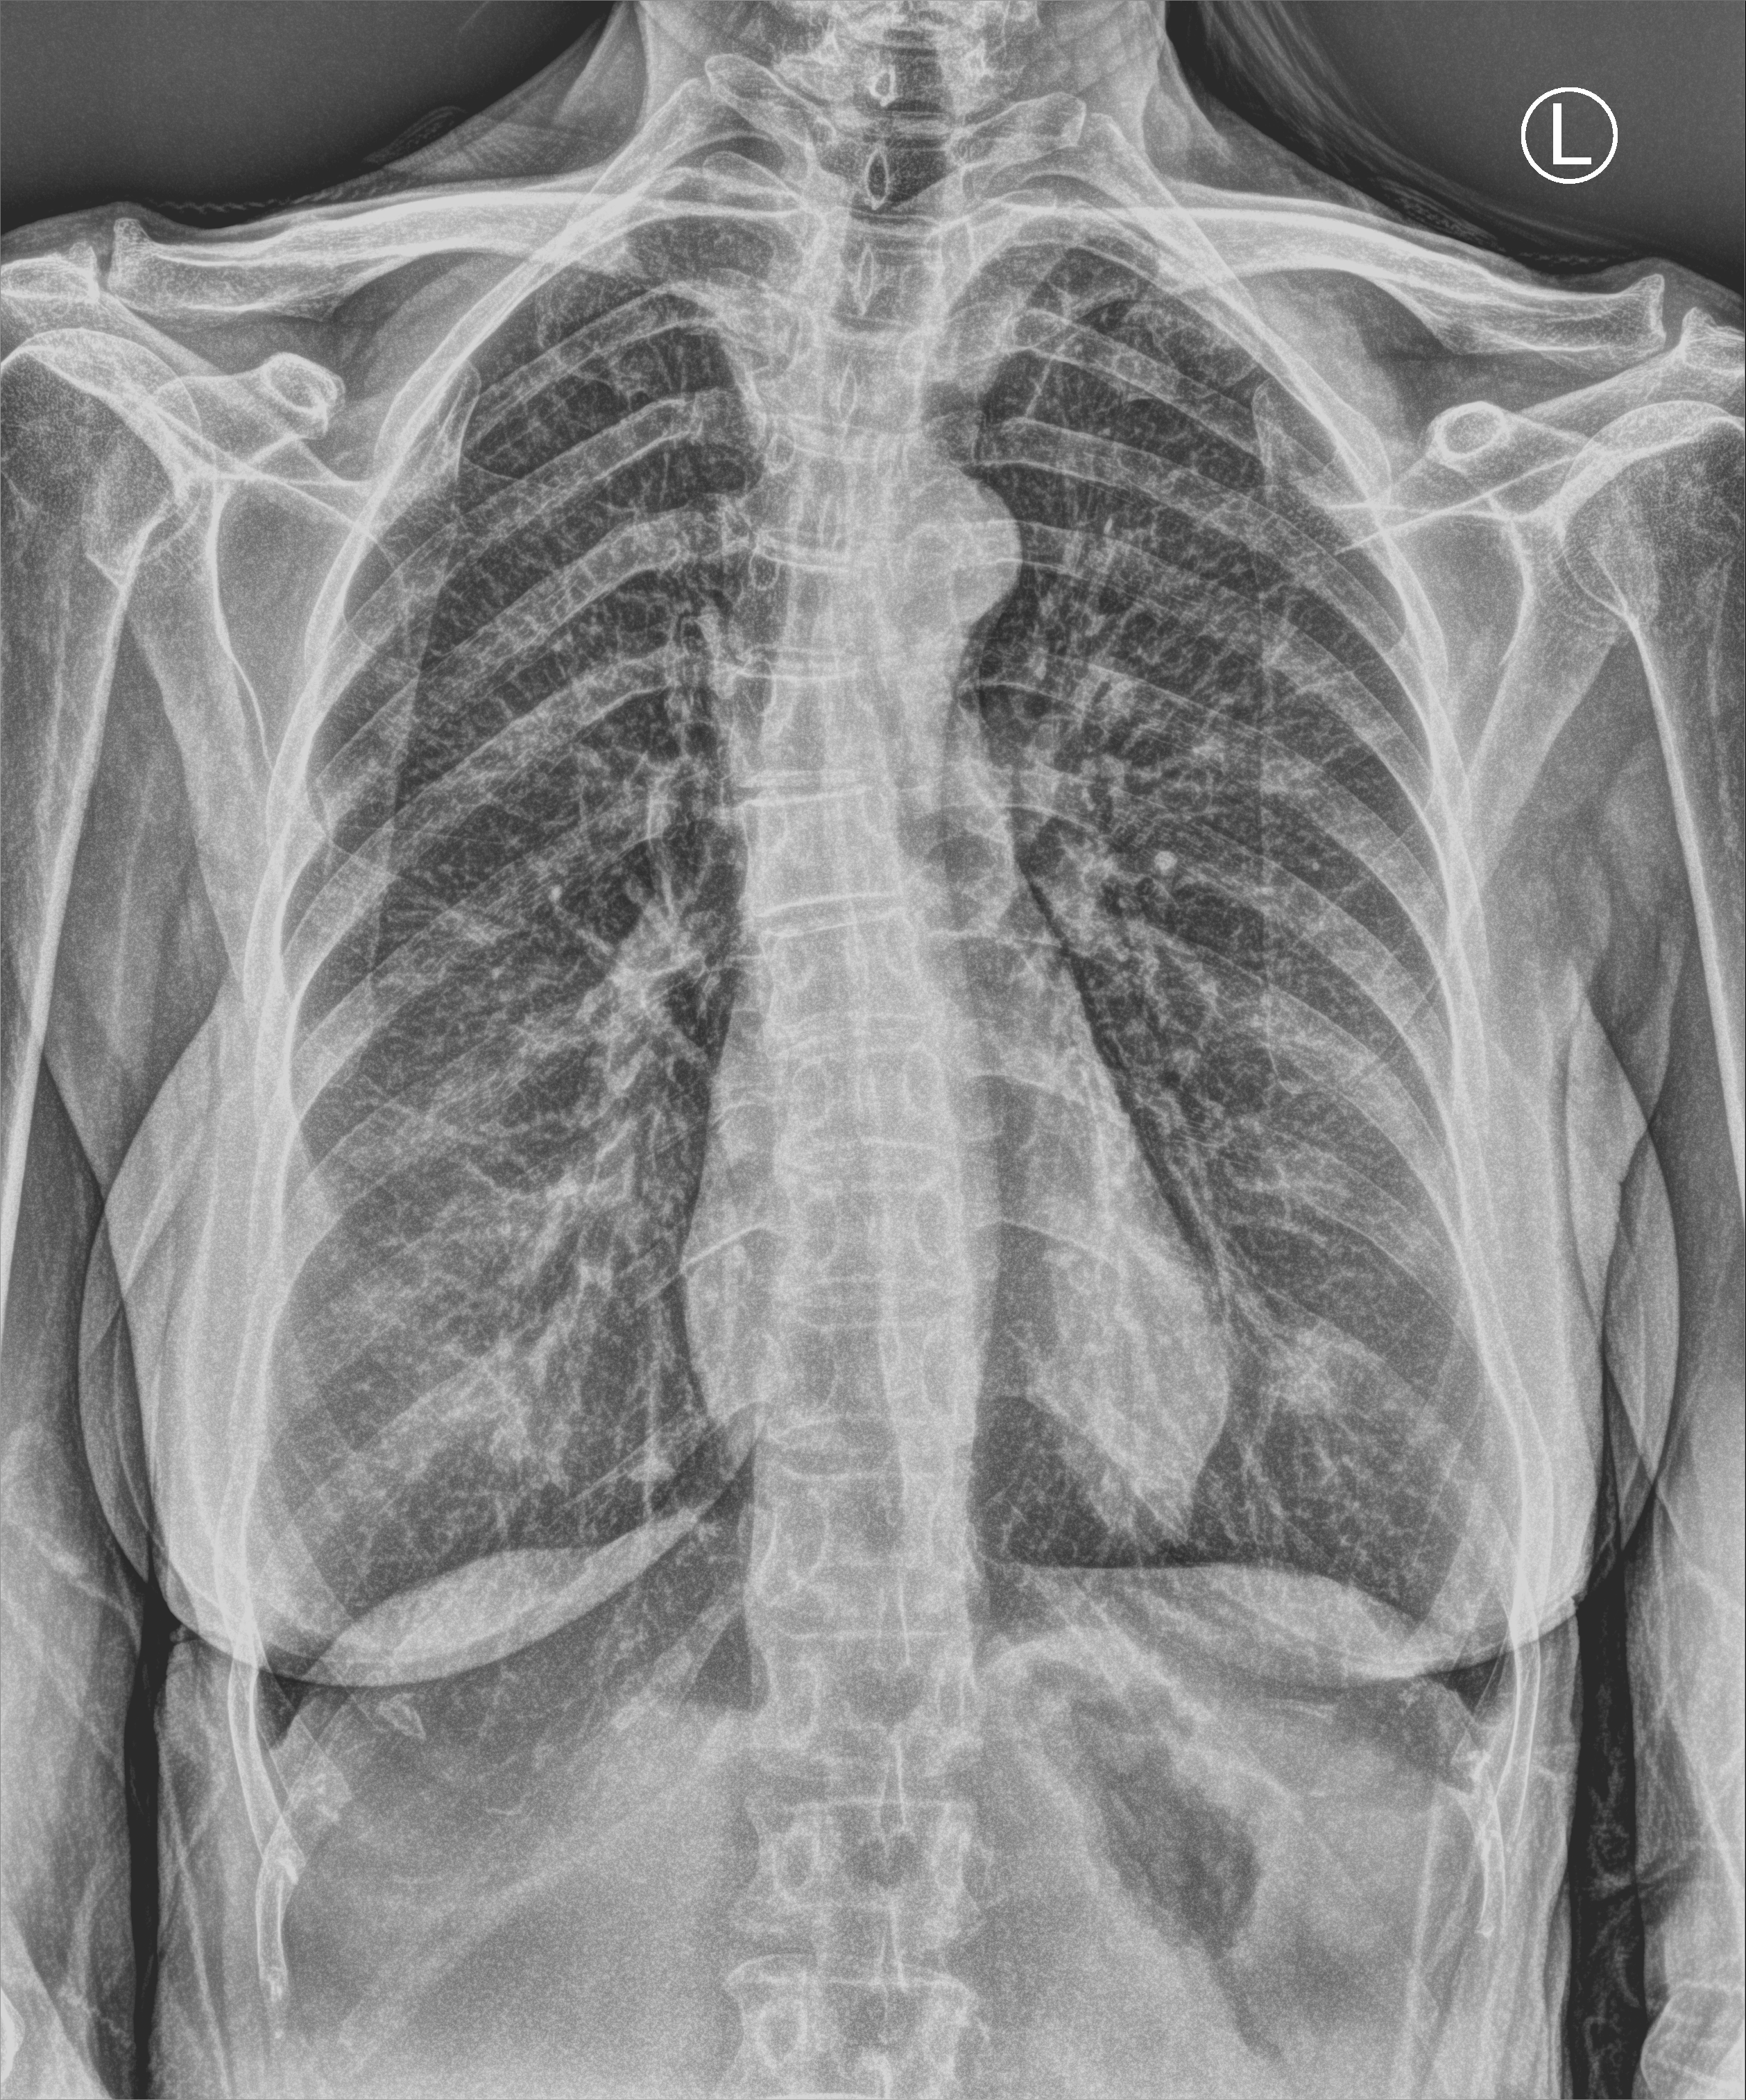
Chest X-ray (portable), anteroposterior (AP) projection. Patient hospitalised with COVID-19; female, aged 60–74 years.
Admission-level facts for this patient (not findings on this image; timing relative to this image not recorded): hypertension (admission record): no.